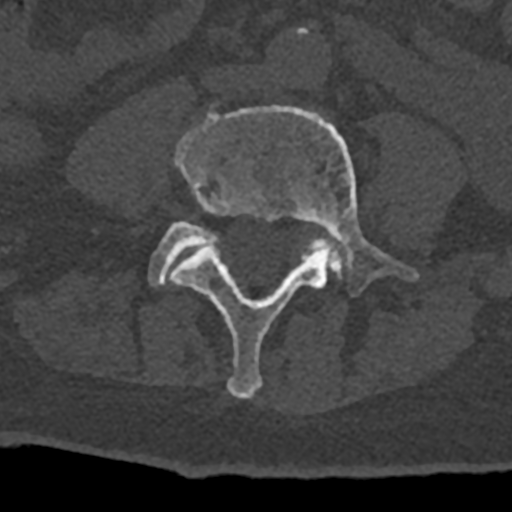
CT including the spine, one axial slice; slice 246 of 797 in the series (ordered by position); reconstruction kernel Br40s/3; bone window (W 1800 / L 400 HU); 0.5 mm slice thickness; 512 × 512 image matrix, field of view 160 × 160 mm. Male patient, age 74 years. From the clinical record (not read from this slice): primary cancer: renal; vertebrae with lytic lesions (as recorded): T10, L1, L2, L3, L4, L5.
Outlined on this slice (semi-automatic segmentation, software-assisted and operator-edited):
- L4 vertebra: bounding box (x1, y1, x2, y2) in pixels: (169, 105, 418, 399)
- L5 vertebra: (148, 222, 341, 286)